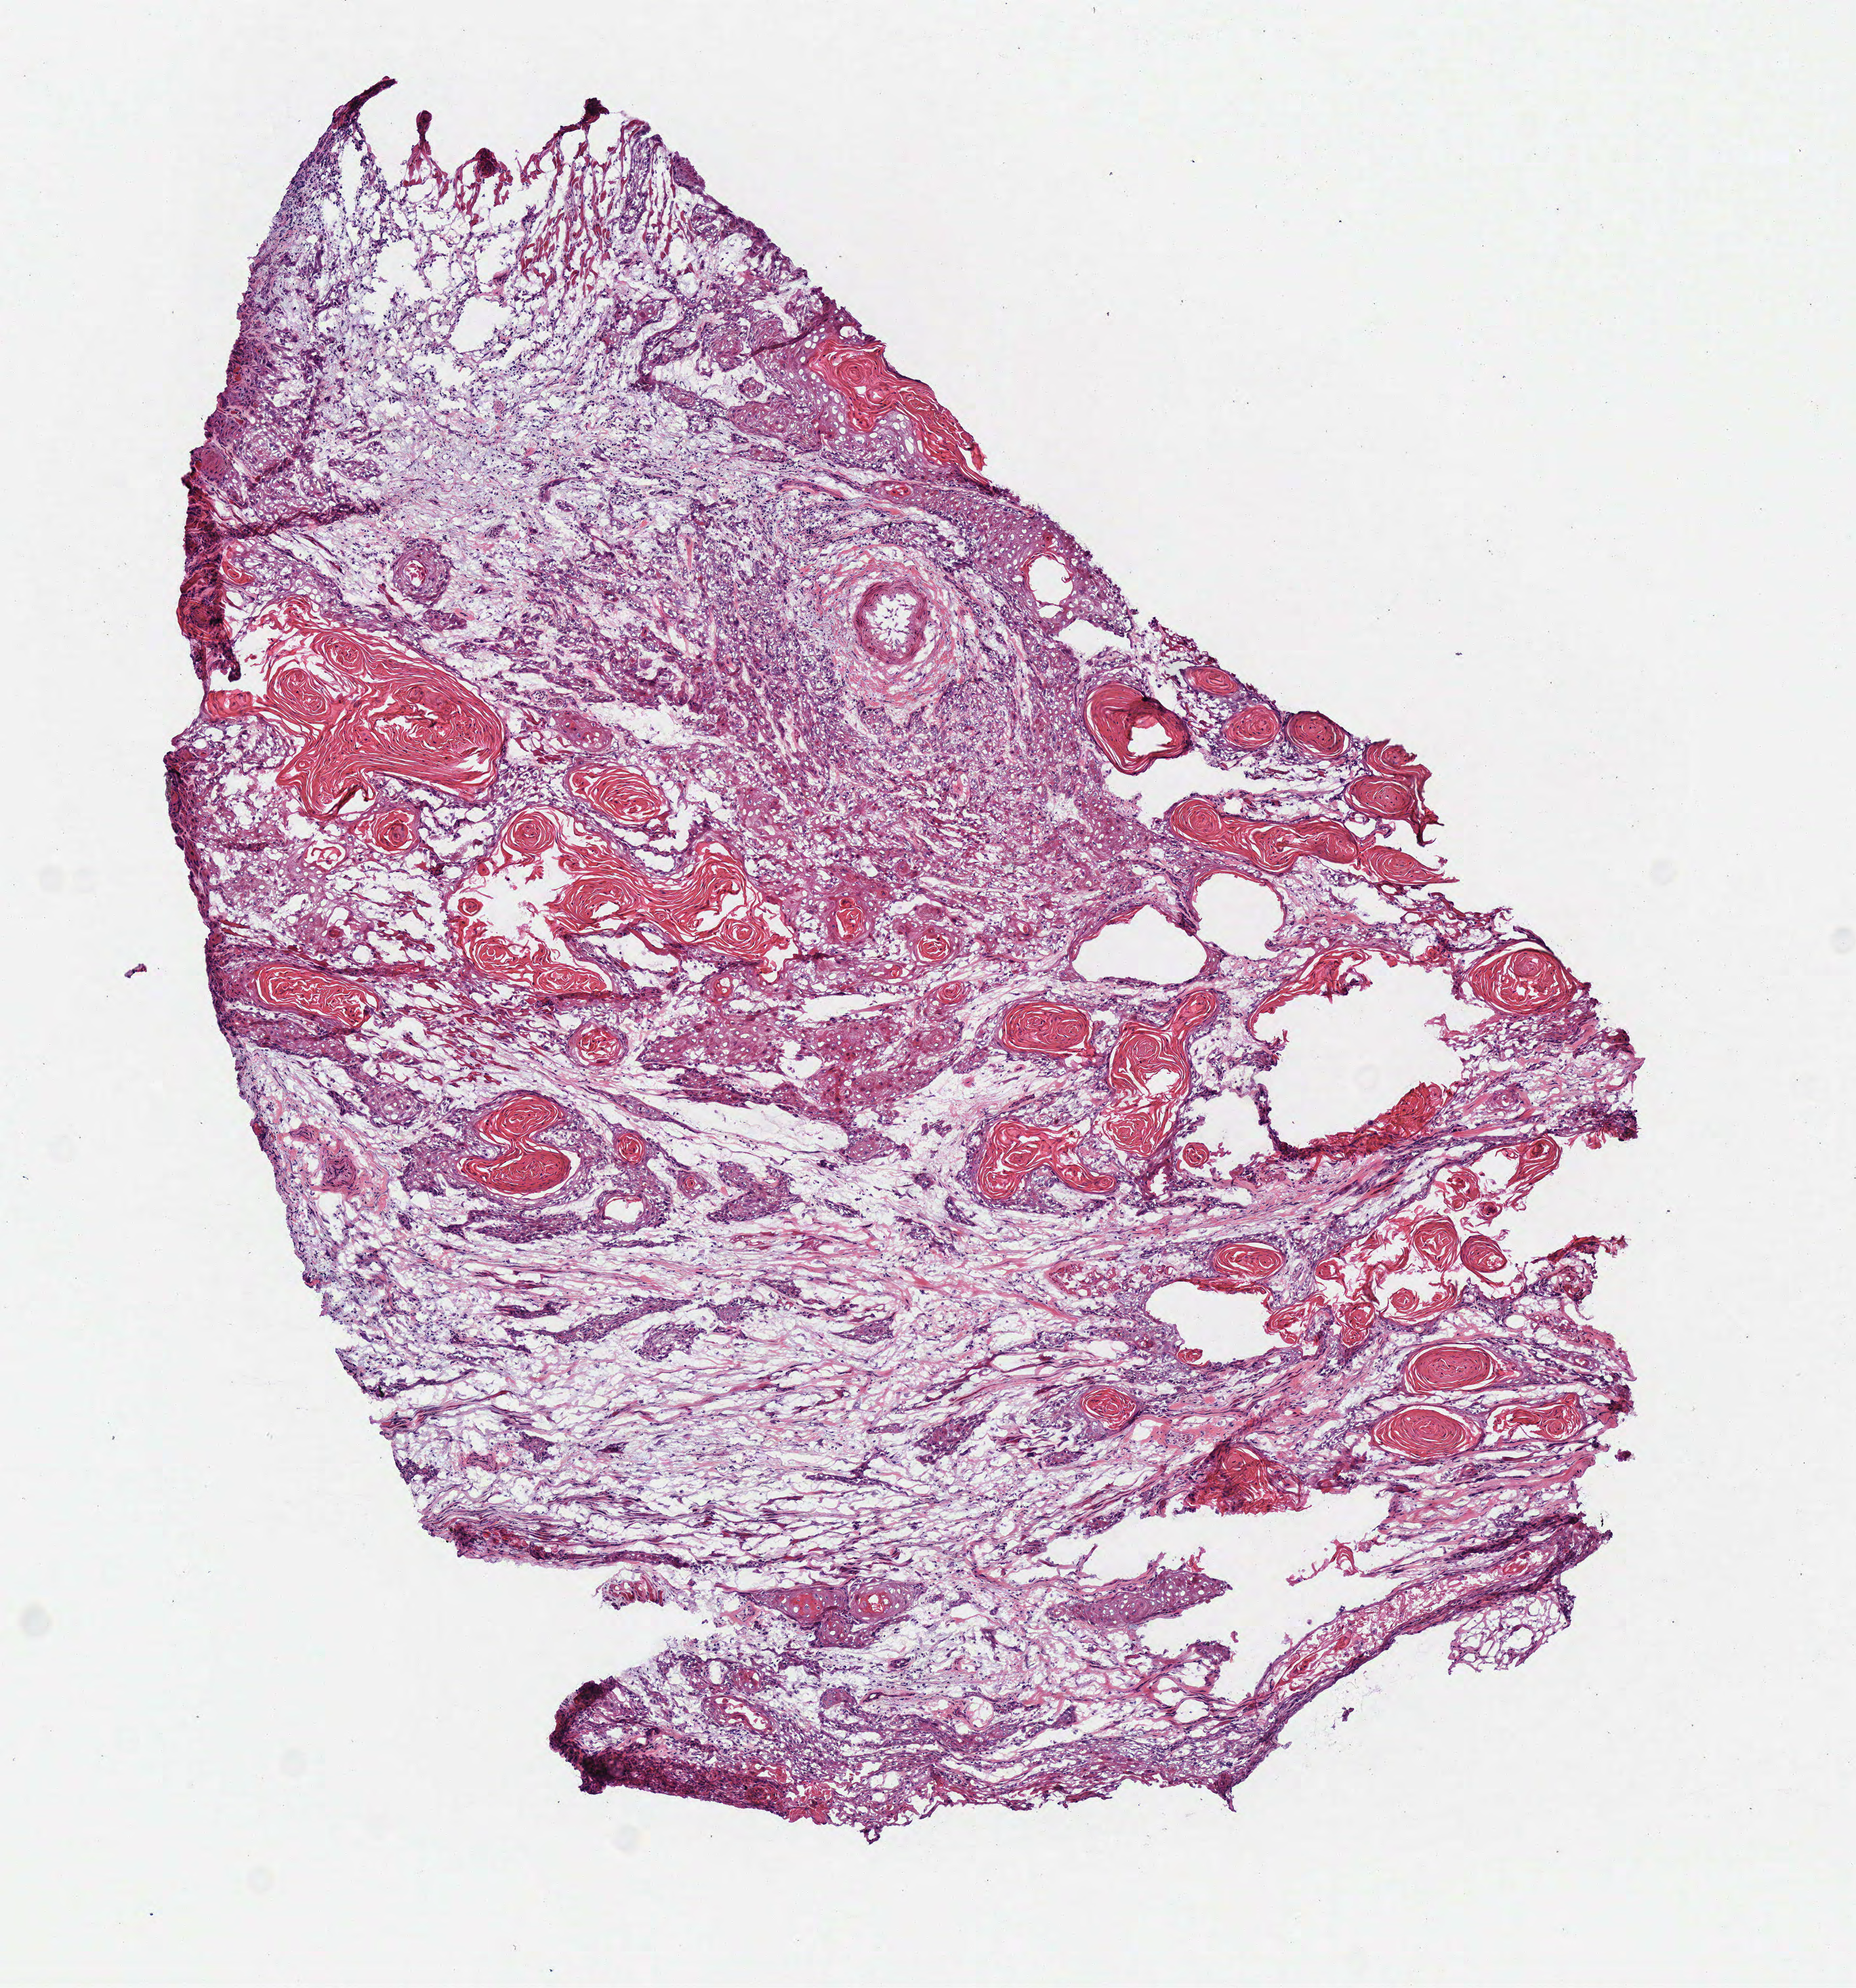
H&E-stained whole-slide image, whole scanned area (about 5.4 x 5.8 mm) shown as a low-resolution overview, frozen section, sample: primary tumour, head and neck. Female patient; age at initial diagnosis 61 years. Histologic grade: G2 (moderately differentiated). Pathologist review of this section (percent, as recorded): tumour cells 60%, tumour nuclei 70%, normal cells 0%, stromal cells 40%, necrosis 0%.
Lymph nodes positive (case pathology): 8 of 30 examined. Diagnosis: Squamous cell carcinoma, keratinizing, NOS (tongue, NOS). AJCC pathologic stage: IVA (7th edition).